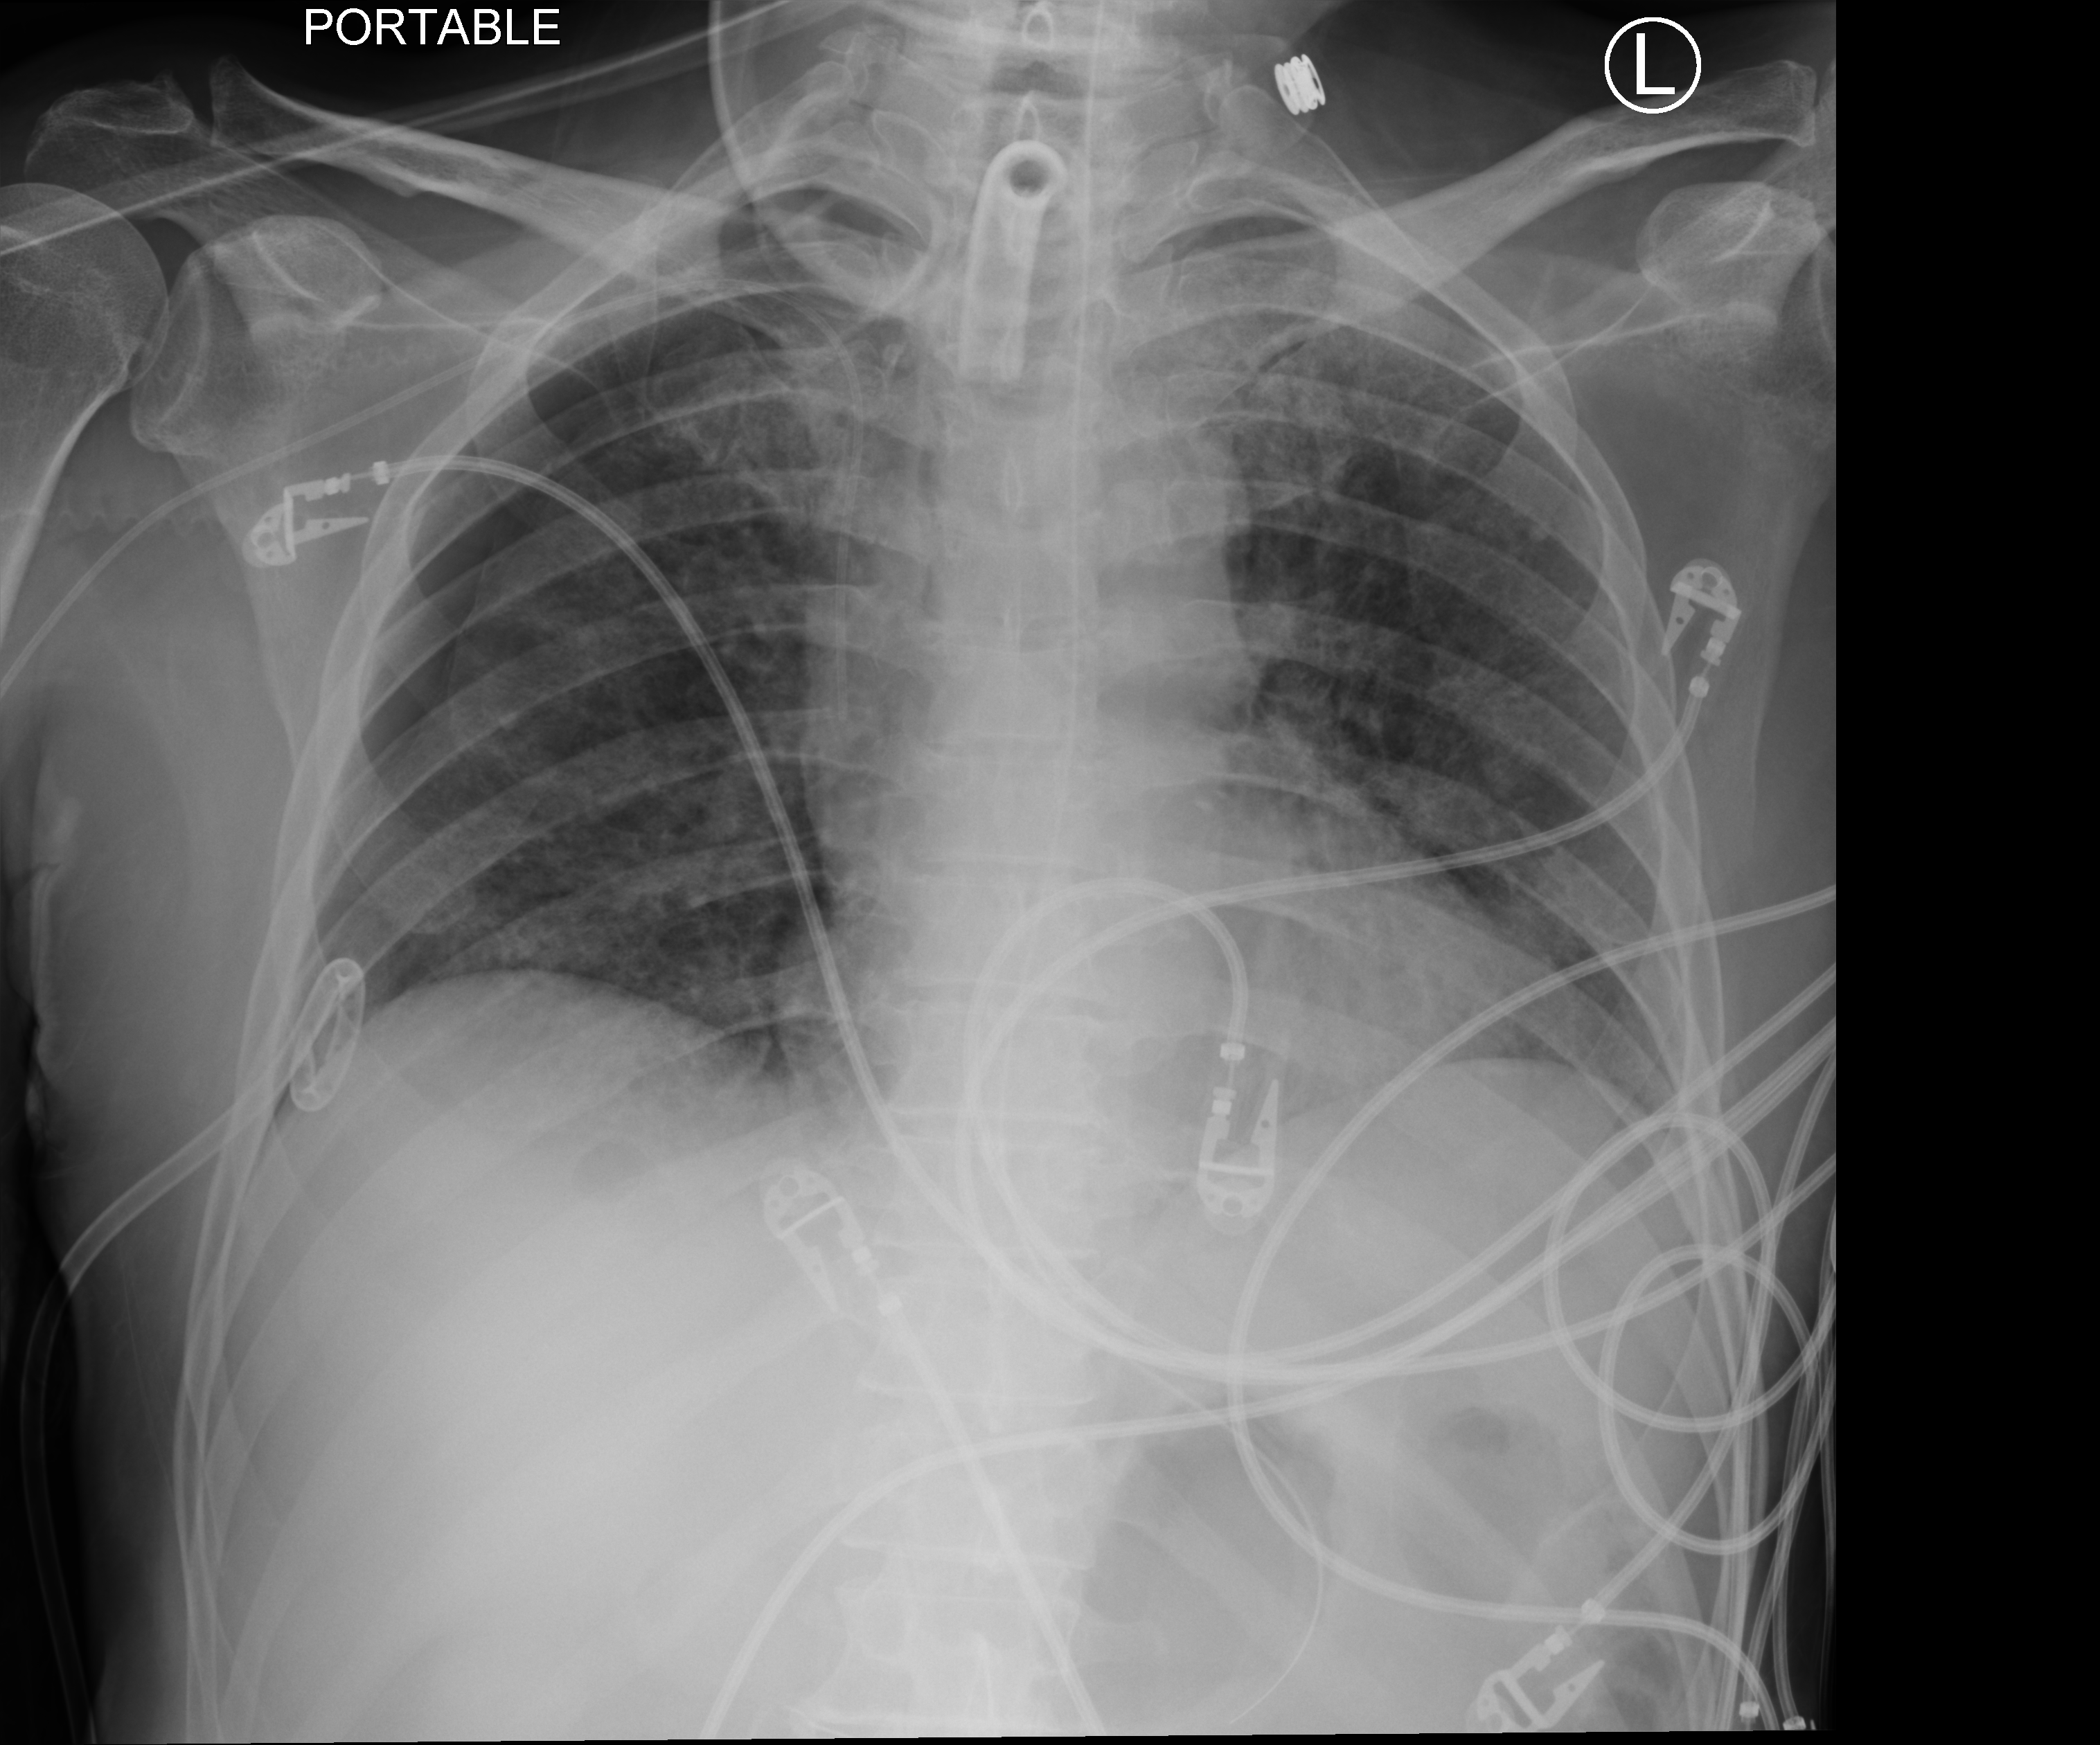
Chest X-ray (portable); anteroposterior (AP) projection. Patient hospitalised with COVID-19; male, aged 18–59 years.
Hospital-stay facts (about this admission, not read from this image; timing relative to this image not recorded): smoking status (admission record): never; mechanically ventilated during this hospital stay: yes.